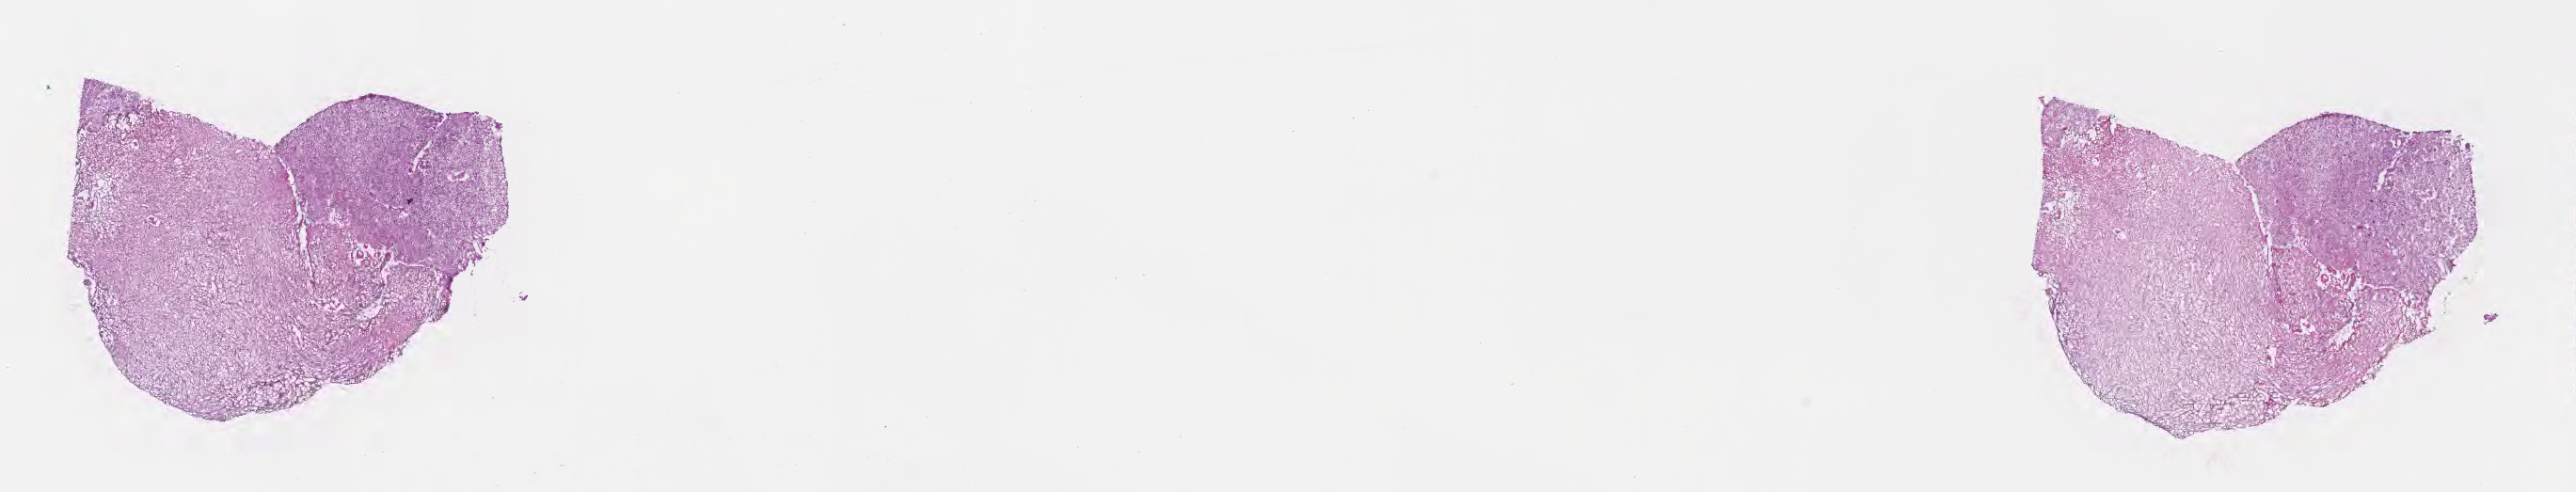
Haematoxylin and eosin whole-slide image, whole scanned area (about 22.1 x 4.2 mm) shown as a low-resolution overview; cryosection; recurrent tumor; site: brain. Male, age 48 years at initial diagnosis. Pathologist review of this section (percent, as recorded): tumor cells 17%, tumor nuclei 68%, stromal cells 8%, necrosis 67%, normal cells 8%. Inflammatory infiltration, as recorded: lymphocyte infiltration 0%, monocyte infiltration 0%, neutrophil infiltration 0%.
Patient diagnosis: Glioblastoma, NOS. Section: bottom of the tissue portion.